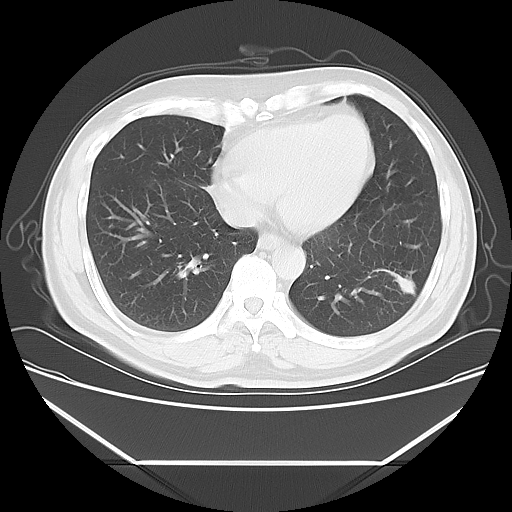
Chest CT, one axial slice; position 20 of 57 along the scan axis; reconstruction kernel LUNG; 120 kVp; lung window (W 1500 / L -600 HU); 5 mm slice thickness; 512 × 512 image matrix, field of view 384 × 384 mm. Male patient, age 53 years. Case-level facts recorded for this patient, not image findings: clinical TNM (as recorded): T1c N0 M0.
Annotated regions visible in this slice (rectangle marked by the reading radiologist):
- lung tumour (recorded histology: adenocarcinoma): bounding box [x1, y1, x2, y2] px = [374, 257, 426, 307]